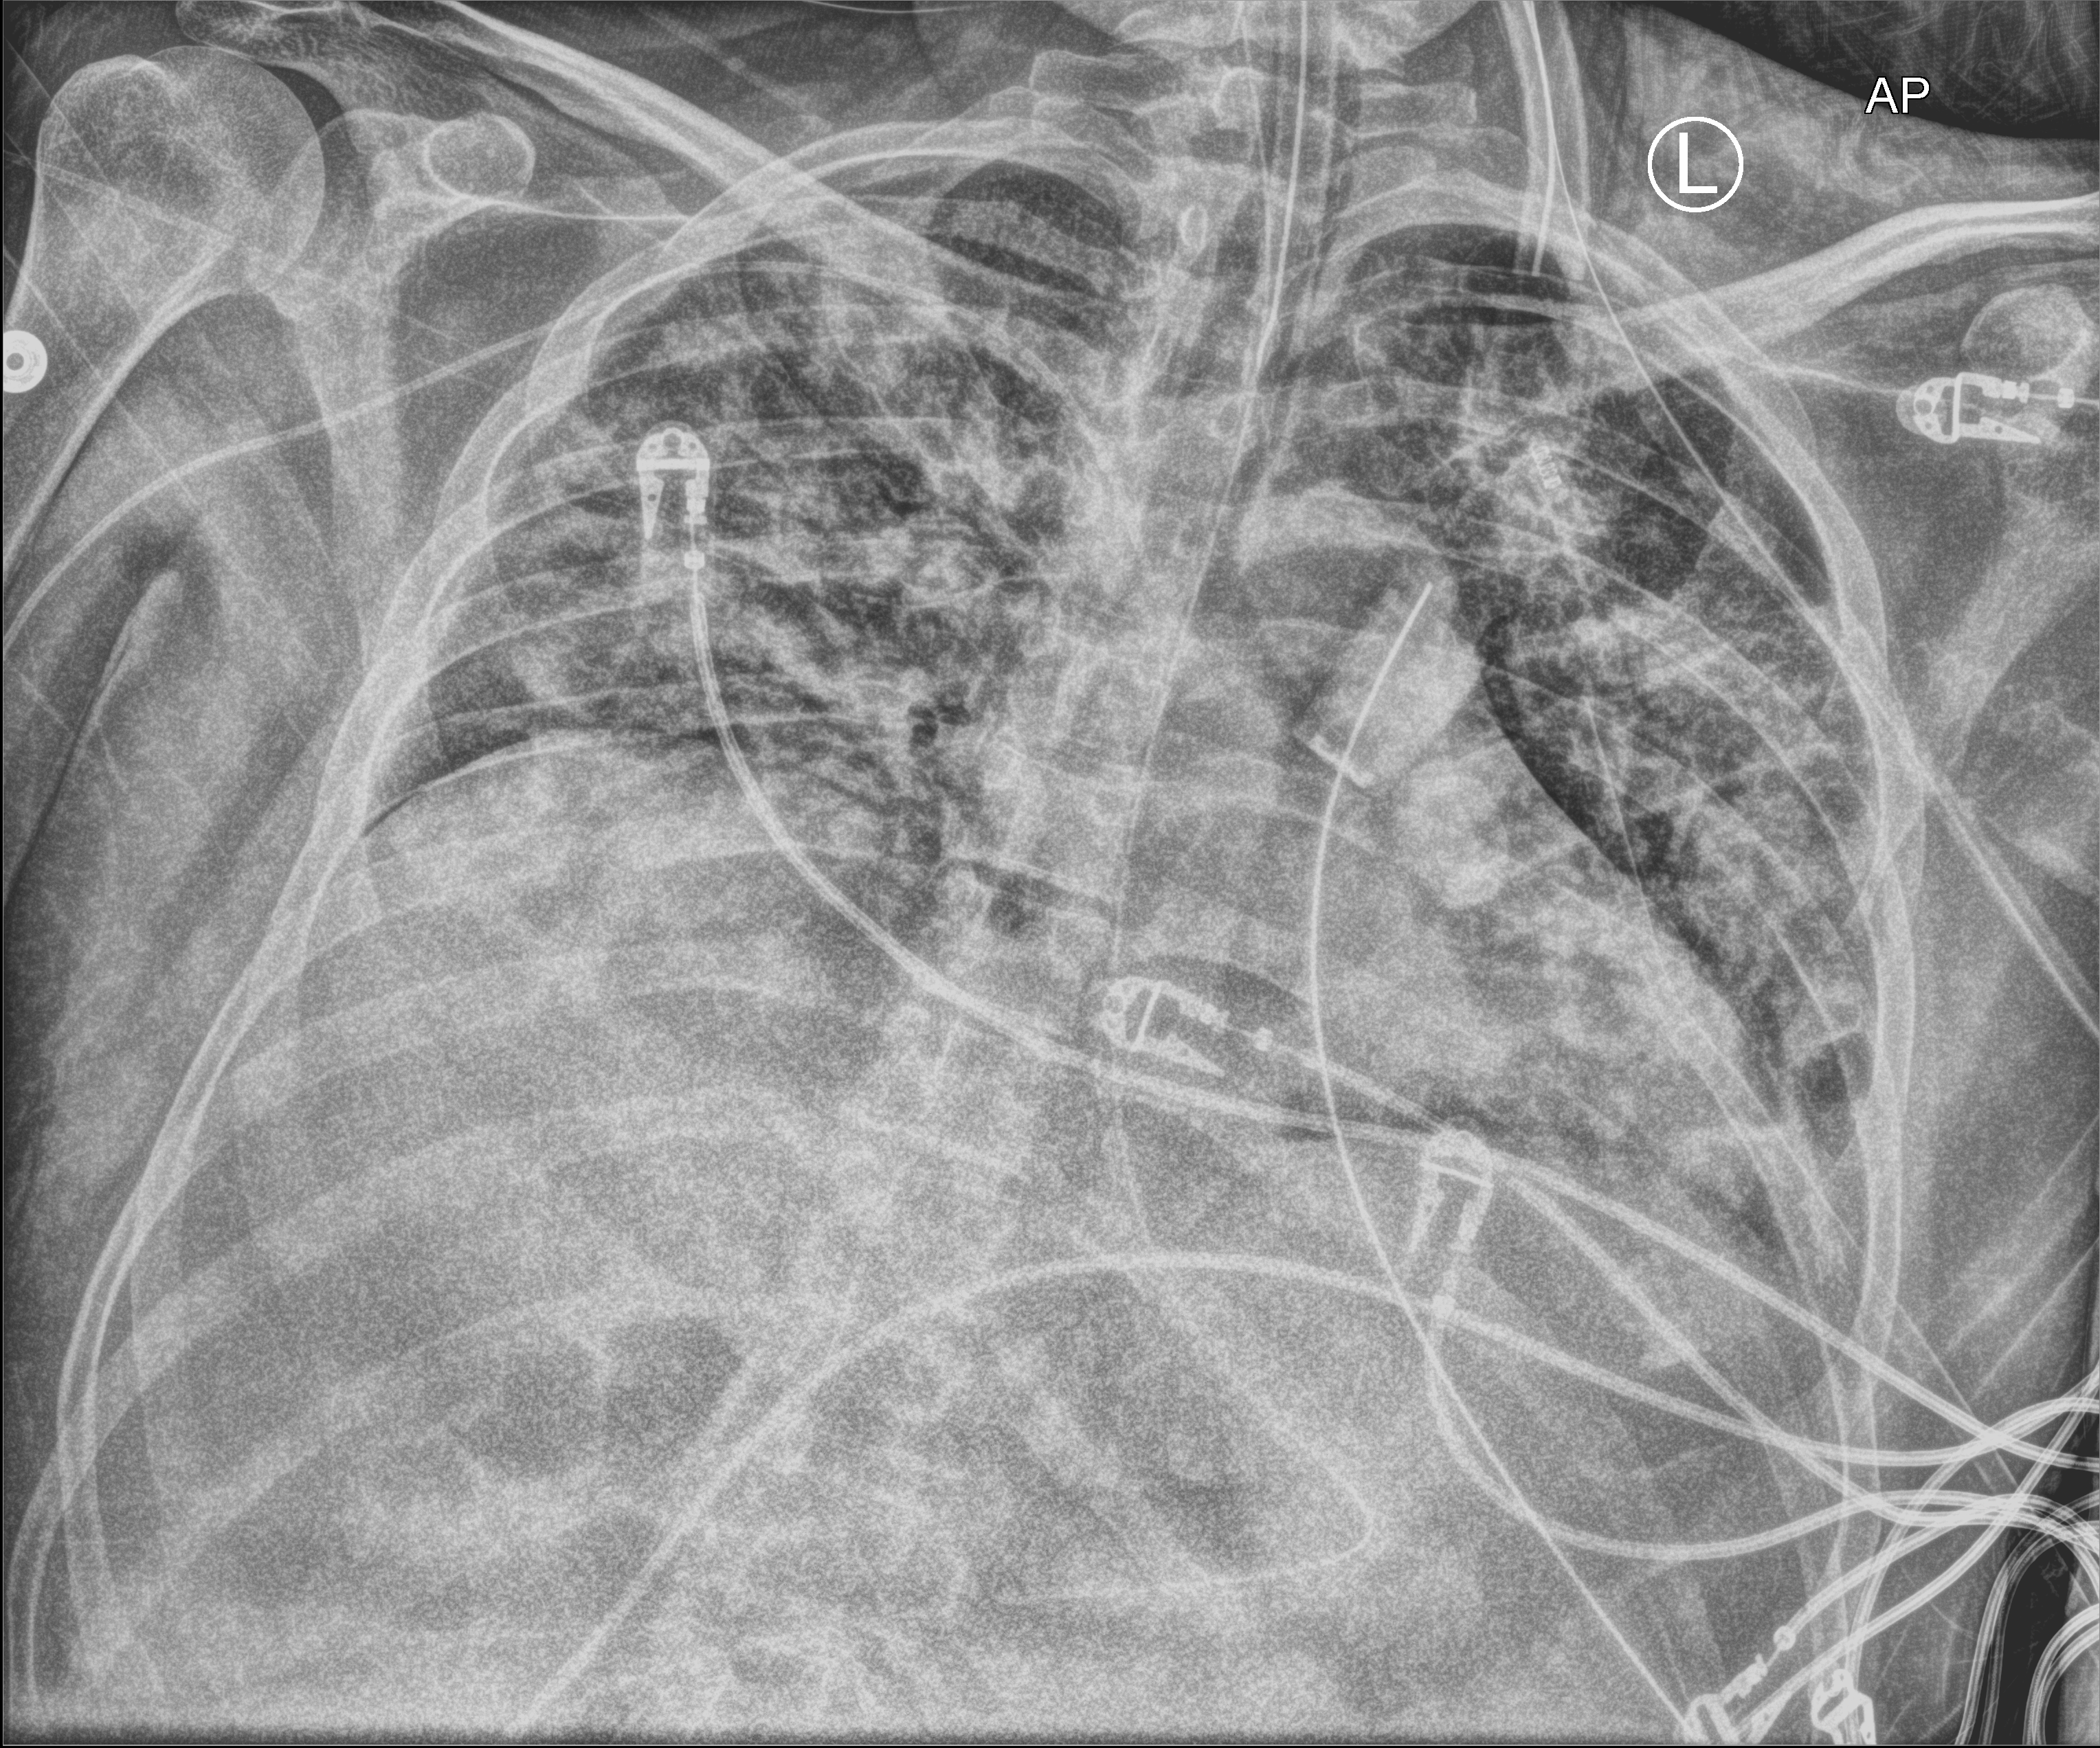
Chest X-ray (portable); anteroposterior (AP) projection. Patient hospitalised with COVID-19; male, aged 18–59 years.
From the hospital-stay record, not from the radiograph (when in the stay this image was taken is not recorded): mechanically ventilated during this hospital stay: yes; diabetes (admission record): no; admitted to intensive care during this hospital stay: yes.